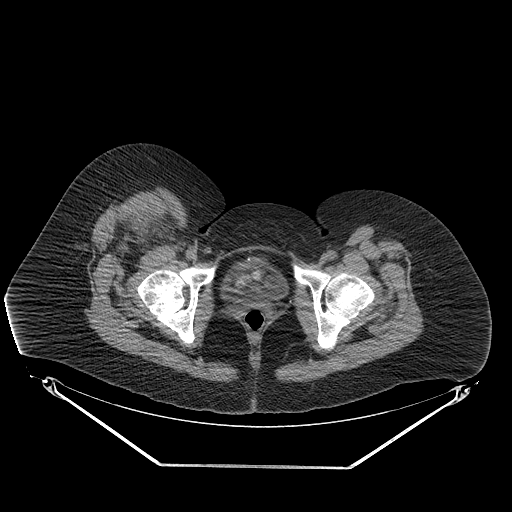
CT of an extremity soft-tissue mass (from a PET/CT study), one axial slice; position 66 of 267 along the scan axis; reconstruction kernel STANDARD; 140 kVp; soft-tissue window (W 400 / L 40 HU); 3.75 mm slice thickness; 512 × 512 image matrix, field of view 500 × 500 mm. Female patient. From the clinical record (not read from this slice): histological type: malignant solitary fibrous tumor; grade: intermediate; site of the primary tumour: right thigh.
Outlined on this slice (expert contour drawn on MRI and transferred to this co-registered scan by the dataset authors):
- gross tumour volume including surrounding oedema: box from (x=107, y=206) to (x=170, y=243) px